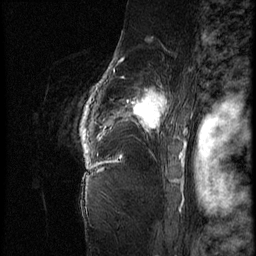
Breast MRI (dynamic contrast-enhanced), one sagittal slice; slice 54 of 62 in the series (ordered by position); 3 images stored at this slice position (order not interpretable as contrast timing); 1.5 T; TE 4.2 ms, TR 9 ms; 2.5 mm slice thickness; 256 × 256 image matrix. Patient: female, 56 years. From the clinical record (not read from this slice): setting: breast cancer imaged before/during neoadjuvant chemotherapy; receptor status: HER2-positive.
Outlined on this slice (semi-automatic segmentation, software-assisted and operator-edited):
- analysis volume of interest (the breast-tissue region the enhancement analysis was run in; not a lesion): box from (x=84, y=75) to (x=181, y=153) px
- tumour enhancement mask (voxels above the 140 % enhancement threshold inside the analysis volume of interest): (x=84, y=89)–(x=168, y=137)